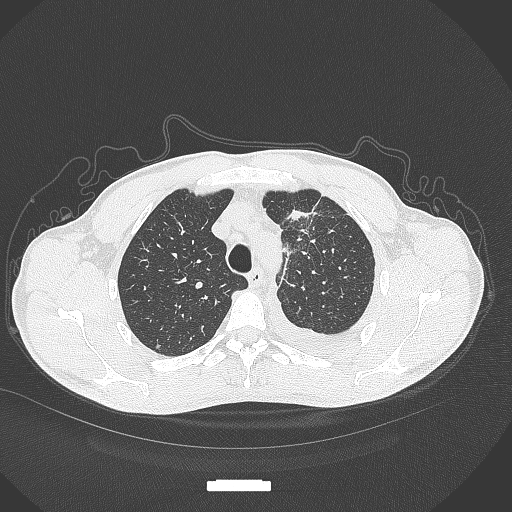
Chest CT, one axial slice; position 271 of 371 along the scan axis; reconstruction kernel B70f; 120 kVp; lung window (W 1500 / L -600 HU); 1 mm slice thickness; 512 × 512 image matrix, field of view 400 × 400 mm. Male patient, age 49 years. Case-level facts recorded for this patient, not image findings: clinical TNM (as recorded): T1c N1 M1.
Structures marked on this image (bounding box drawn by a radiologist):
- lung tumour (recorded histology: adenocarcinoma): bounding box (x1, y1, x2, y2) in pixels: (282, 209, 325, 232)